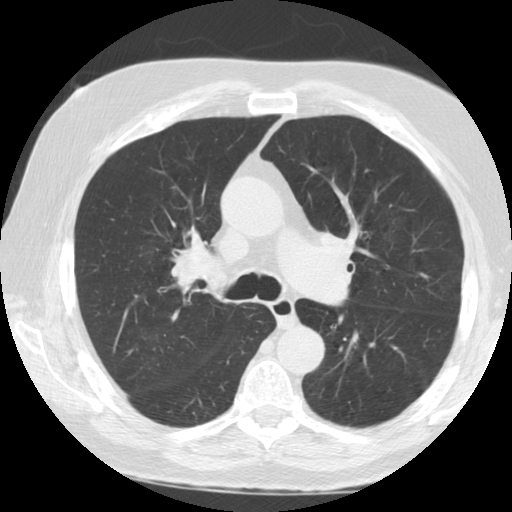
Axial slice from a low-dose chest CT screening exam, second screening round (one year after baseline), lung window (W 1500 / L -600 HU), 2.5 mm slice thickness, 512 × 512 image matrix. Male participant, aged 72 years at enrolment. Former smoker at enrolment.
Expert reader's lesion annotation, bounding box <161,229,229,300> (left, top, right, bottom; pixels). No non-calcified nodule or mass ≥4 mm was recorded by the screening reader at this exam. Official screen result: negative screen, minor abnormalities not suspicious for lung cancer. Participant outcome: lung cancer diagnosed 415 days after this screen — small cell carcinoma, NOS, right upper lobe, stage IV (AJCC 6th edition), 7 mm at pathology.